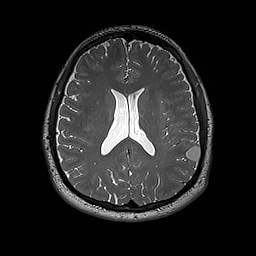
Brain MRI from a brain-tumour surgery series, one axial slice. Slice 84 of 192 in the series (ordered by position). 256 × 256 image matrix, field of view 250 × 250 mm. Case-level facts recorded for this patient, not image findings: histopathology: Dysembryoplastic neuroepithelial tumor; WHO grade: 1; IDH mutation: no; tumour location: Left Inferior Parietal.
Annotated regions visible in this slice (expert manual segmentation):
- tumour: bounding box <186,146,201,163> (left, top, right, bottom; pixels)